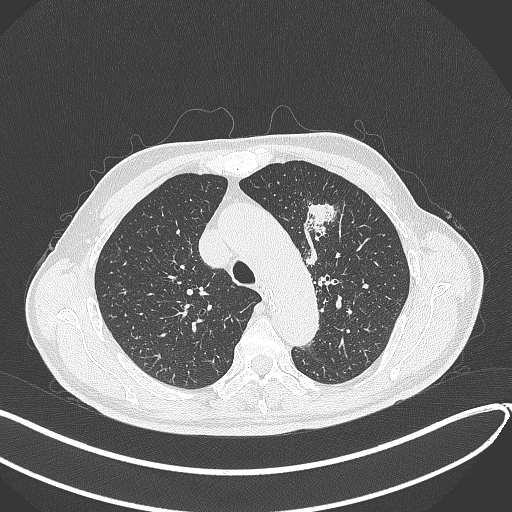
Chest CT, one axial slice. Slice 308 of 459 in the series (ordered by position). 120 kVp. Lung window (W 1500 / L -600 HU). 512 × 512 image matrix, field of view 400 × 400 mm. Patient: male, 74 years. From the clinical record (not read from this slice): clinical TNM (as recorded): T2b N0 M1c.
Annotated regions visible in this slice (bounding box drawn by a radiologist):
- lung tumour (recorded histology: adenocarcinoma): box from (x=306, y=200) to (x=338, y=239) px